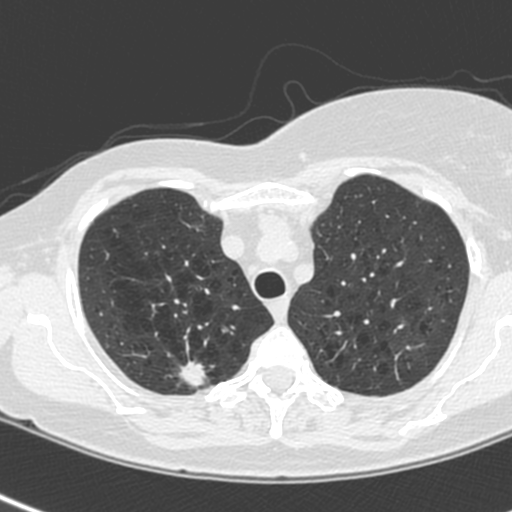
Axial slice from a low-dose chest CT screening exam. First (baseline) screen. Lung window (W 1500 / L -600 HU). 1.3 mm slice thickness. 120 kVp. Slice 37 of 214 in the series. Female participant, aged 64 years at enrolment. Current smoker at enrolment.
- Expert-annotated lung lesion, bounding box (x1, y1, x2, y2) in pixels: (166, 353, 221, 403).
- Screening reader's record for this exam (one nodule recorded; not confirmed to be the boxed lesion): non-calcified nodule or mass ≥4 mm, right upper lobe, 13 × 10 mm, spiculated (stellate) margins, soft tissue attenuation.
- Official screen result: positive, change unspecified: nodule(s) >= 4 mm or enlarging nodule(s), mass(es), or other non-specific abnormalities suspicious for lung cancer.
- Participant outcome: lung cancer diagnosed 21 days after this screen — adenocarcinoma, NOS, right upper lobe, poorly differentiated (G3), stage IIIB (AJCC 6th edition), 20 mm at pathology.